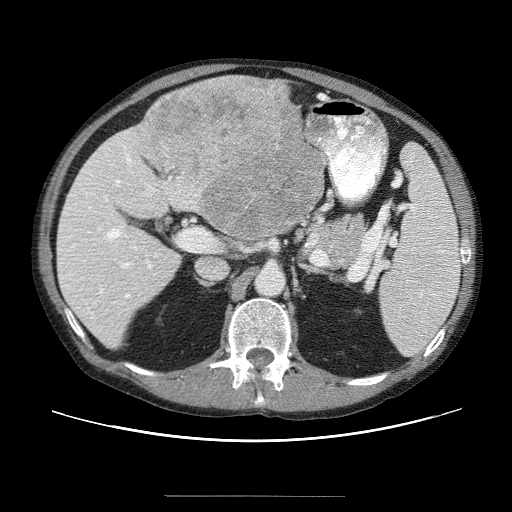
Contrast-enhanced abdominal CT (liver protocol), one axial slice; position 22 of 69 along the scan axis; 120 kVp; soft-tissue window (W 400 / L 40 HU); 512 × 512 image matrix. From the clinical record (not read from this slice): diagnosis: hepatocellular carcinoma (patient treated with transarterial chemoembolisation; whether this scan precedes or follows treatment is not stated here); TNM stage (as recorded): Stage-IVB.
Annotated regions visible in this slice (semi-automatic segmentation, software-assisted and operator-edited):
- liver parenchyma outside the tumour (the mass and vessels are separate outlines, so this box may not span the whole liver): bounding box (x1, y1, x2, y2) in pixels: (56, 78, 324, 344)
- mass: (136, 78, 324, 244)
- liver vessels: (62, 156, 177, 327)